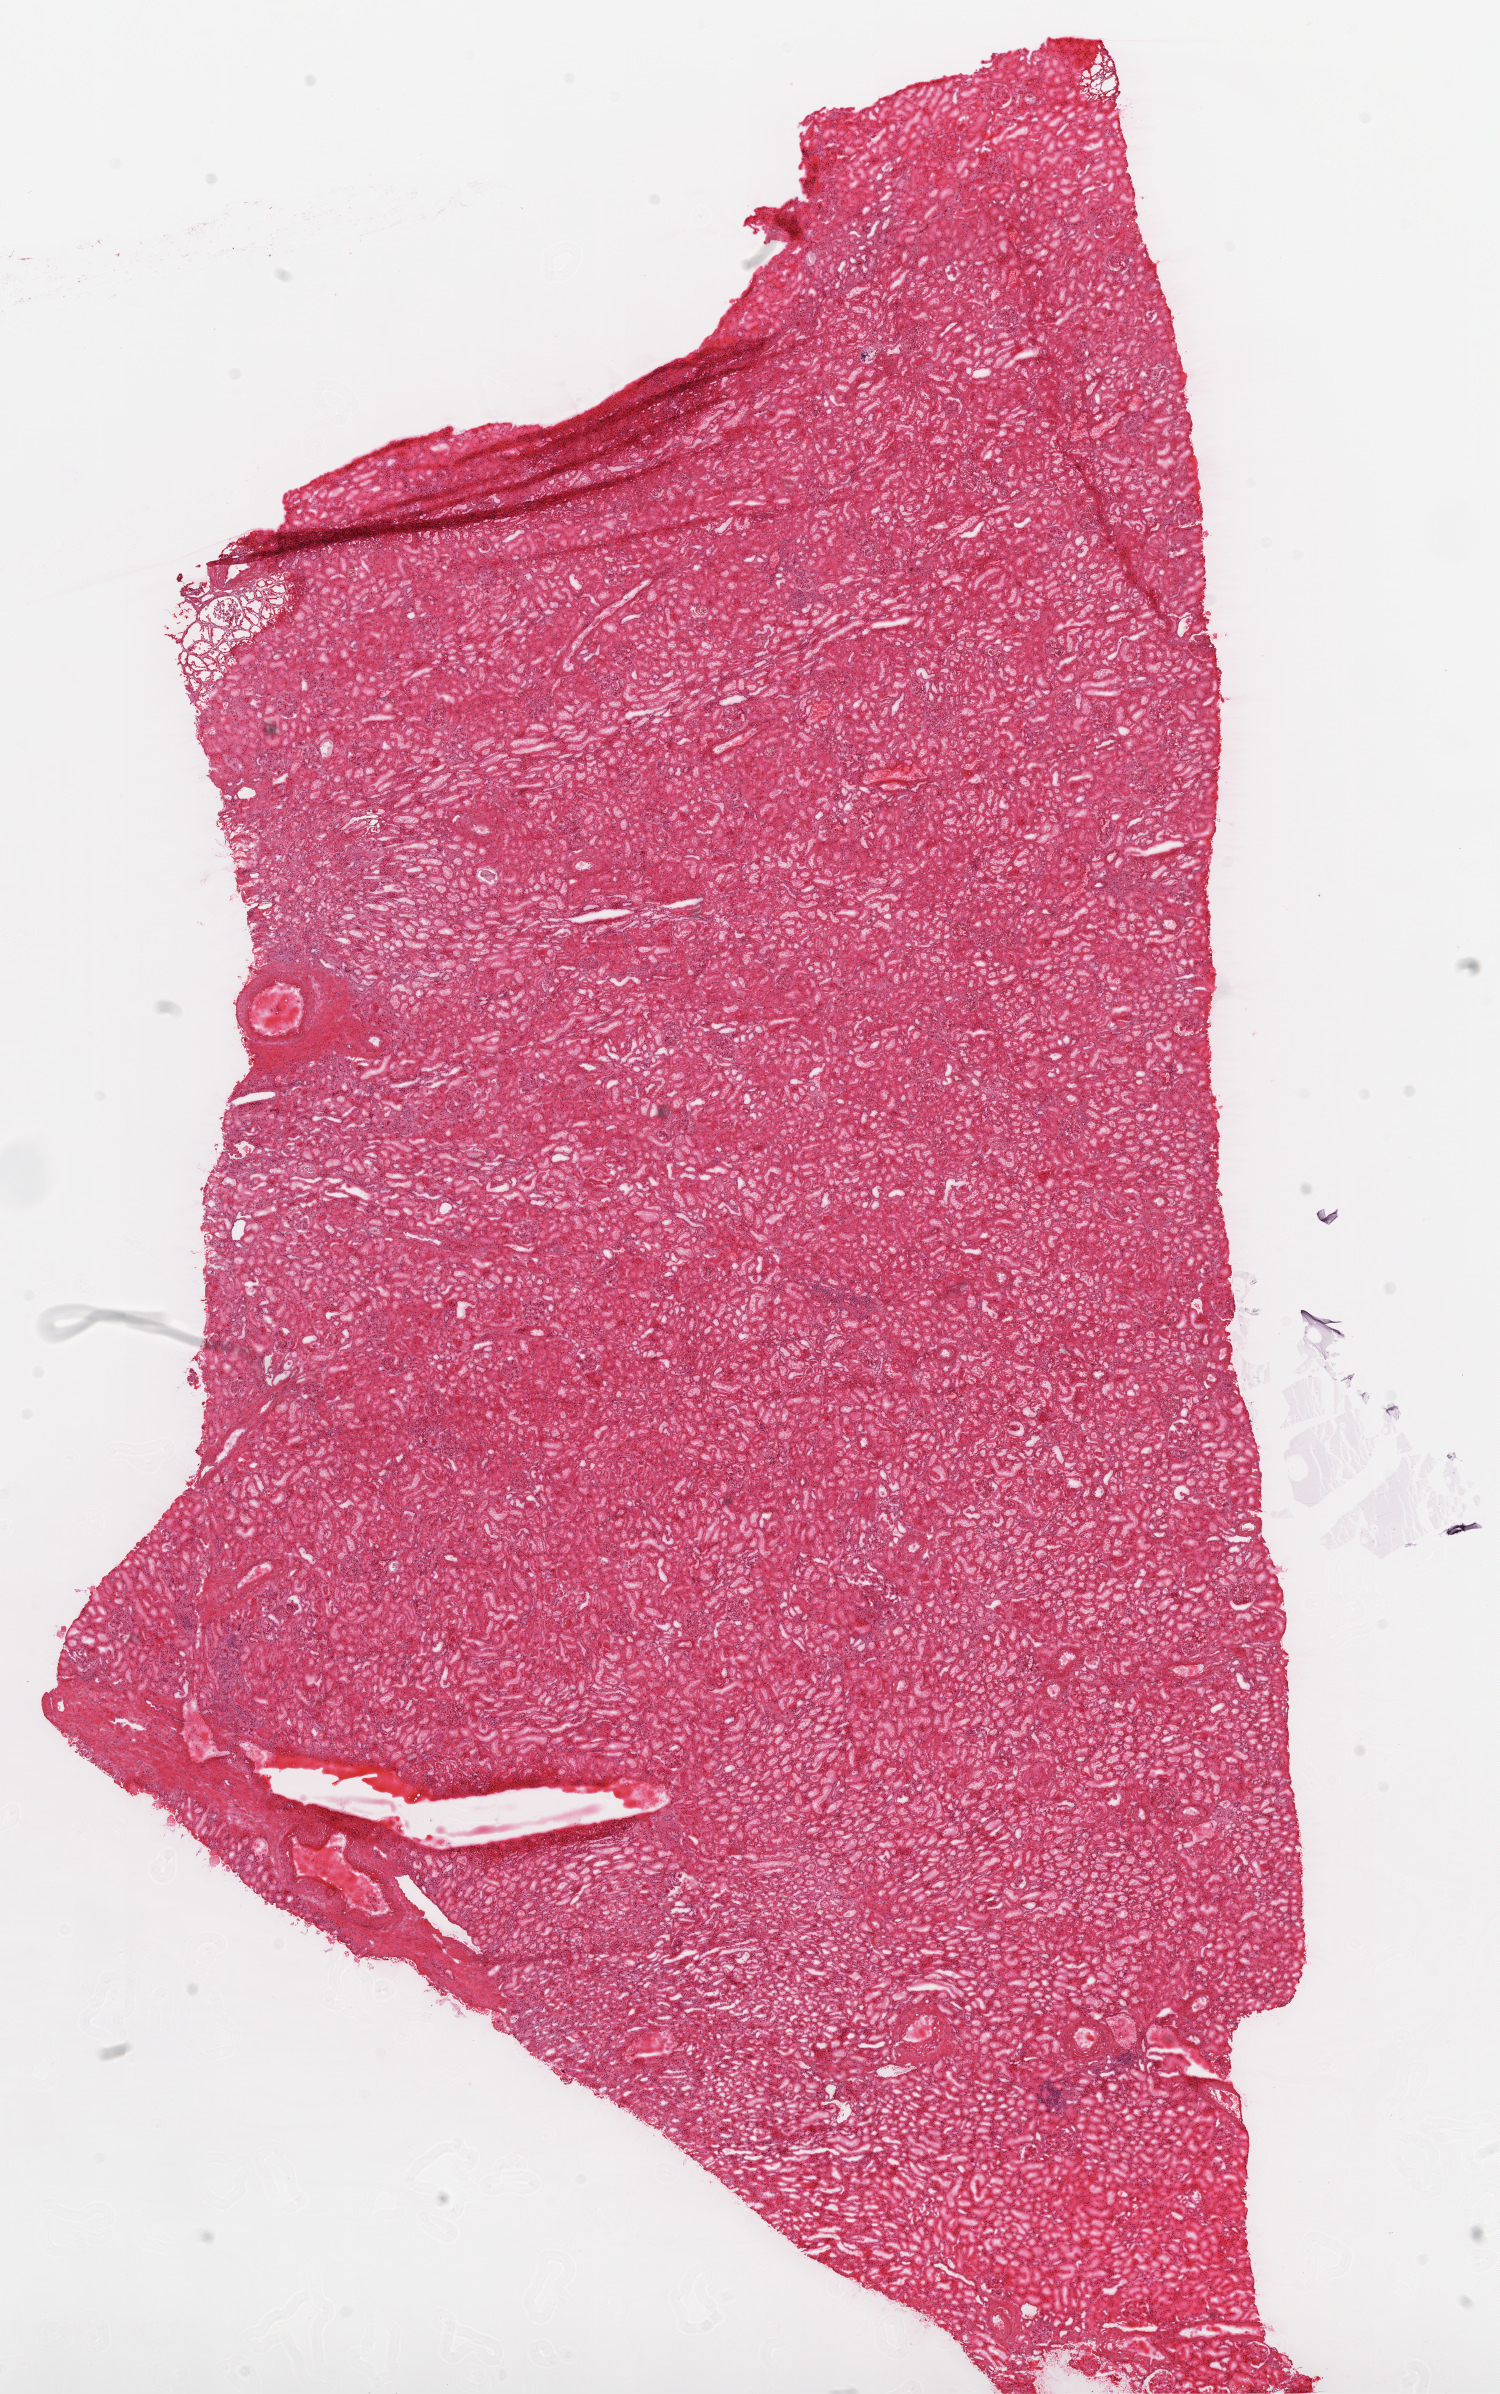
H&E whole-slide image, a low-resolution overview of the entire scanned area, about 12.0 x 19.2 mm, frozen section from the top of the tissue portion, solid tissue normal (non-tumour tissue) sample from the kidney. Male patient; age at initial diagnosis 69 years.
- this section: solid tissue normal (non-tumour) sample from the same patient
- patient diagnosis: Clear cell adenocarcinoma, NOS